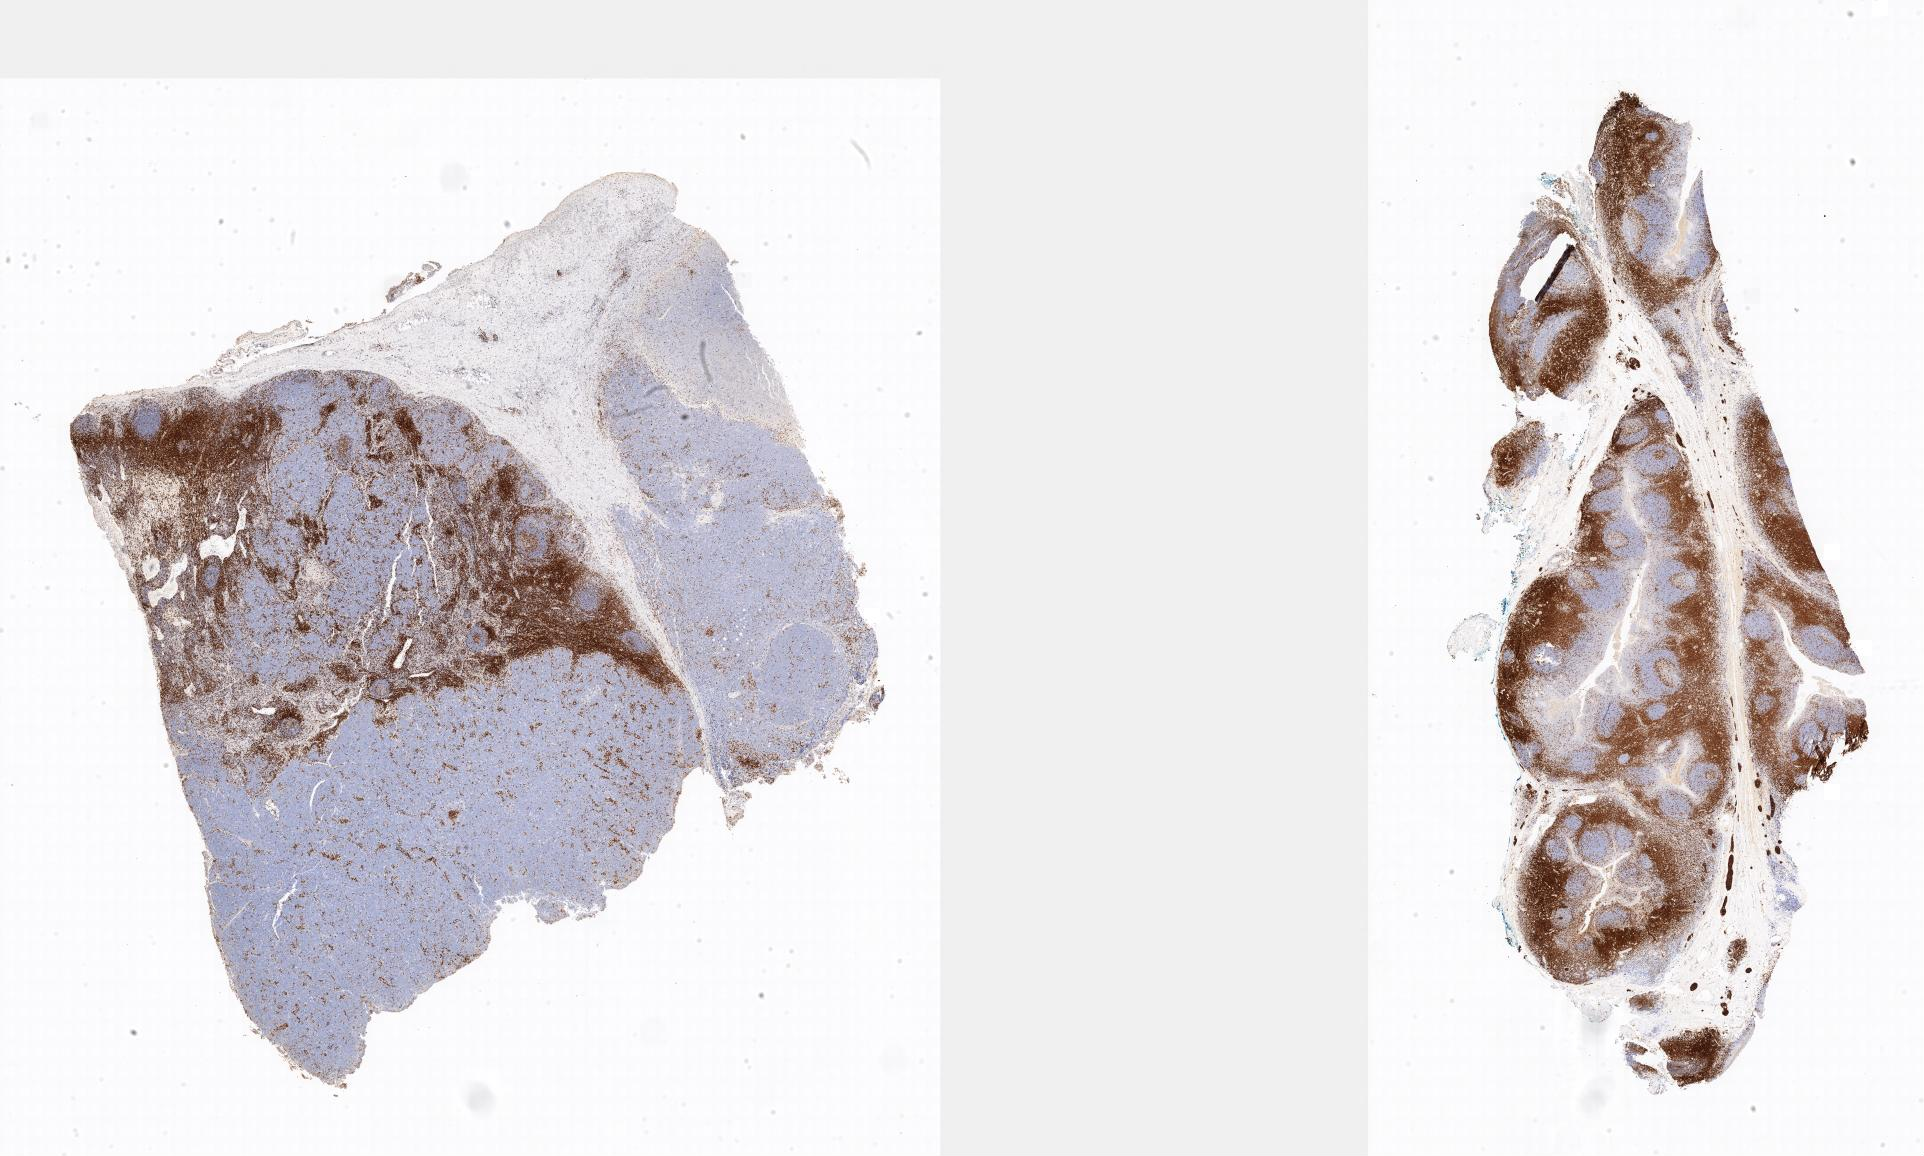
Immunohistochemistry (IHC) whole-slide image stained for CD3 — shown as a low-resolution overview of the whole scanned area; tumor tissue; anatomic site: abdominal lymph node. Patient female; aged 14.
• diagnosis: Burkitt lymphoma, NOS